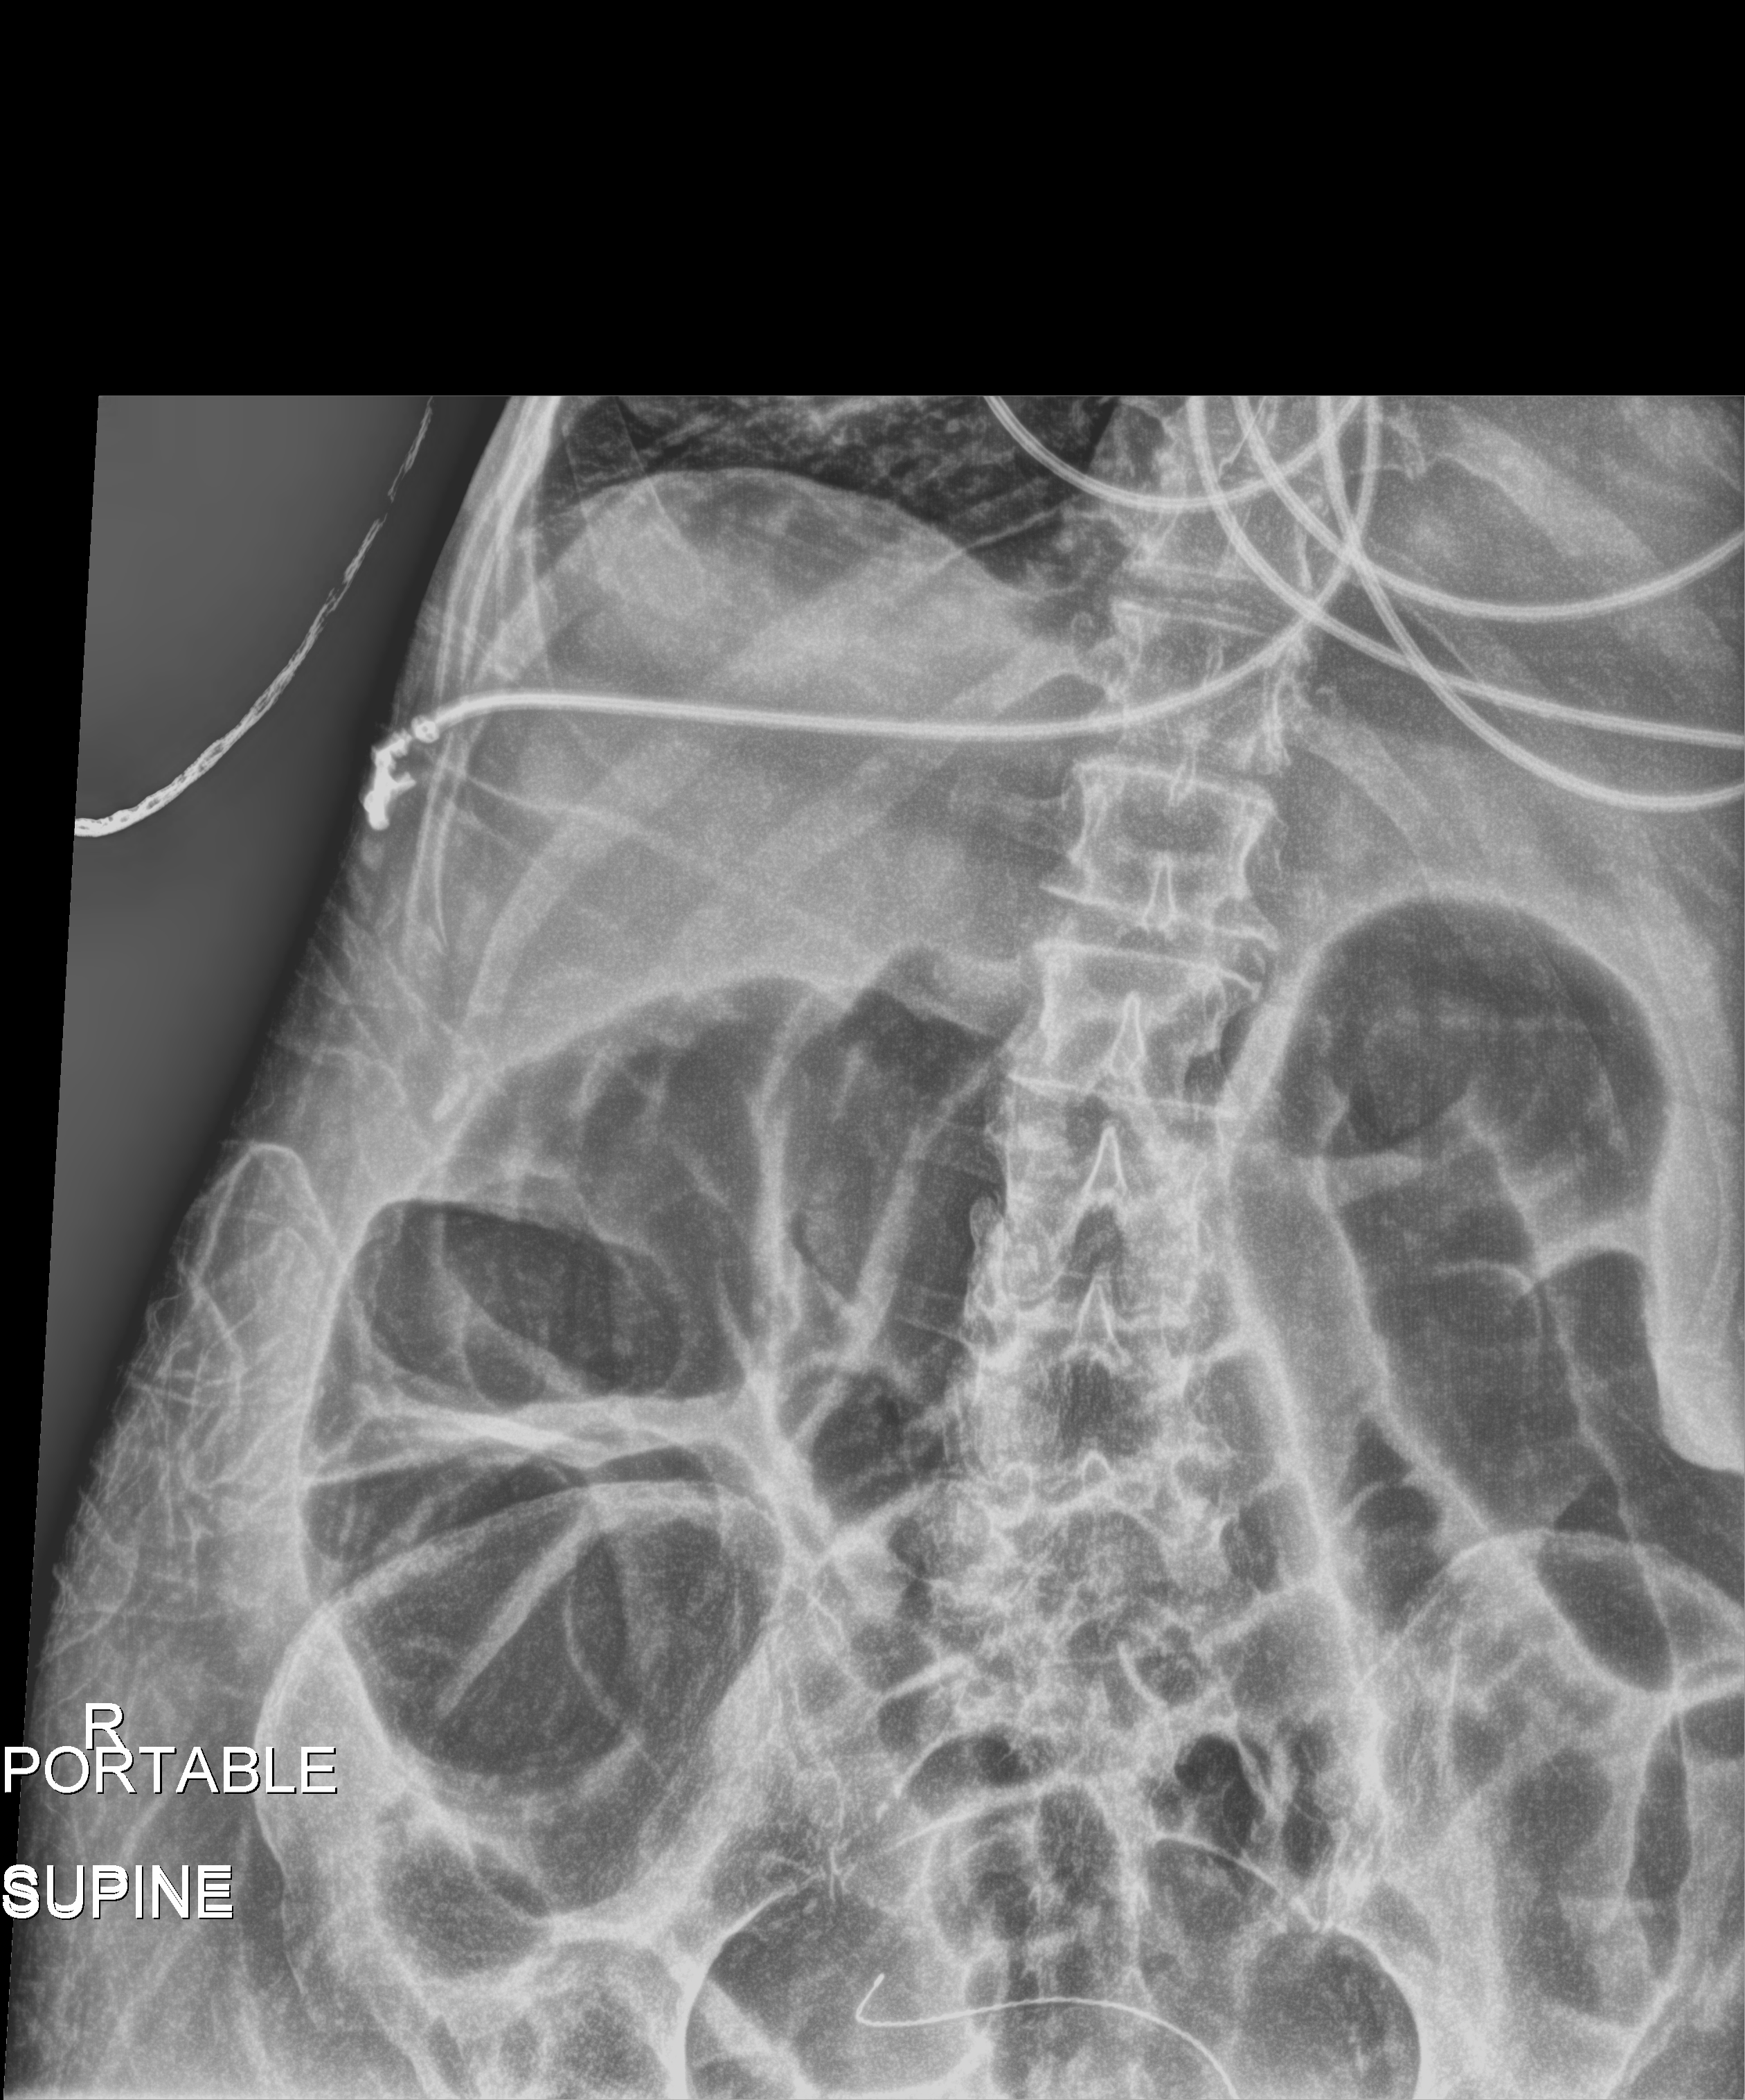
Portable abdomen radiograph, anteroposterior (AP) projection. Patient hospitalised with COVID-19; female, aged 60–74 years.
Admission-level facts for this patient (not findings on this image; timing relative to this image not recorded): admitted to intensive care during this hospital stay: yes.